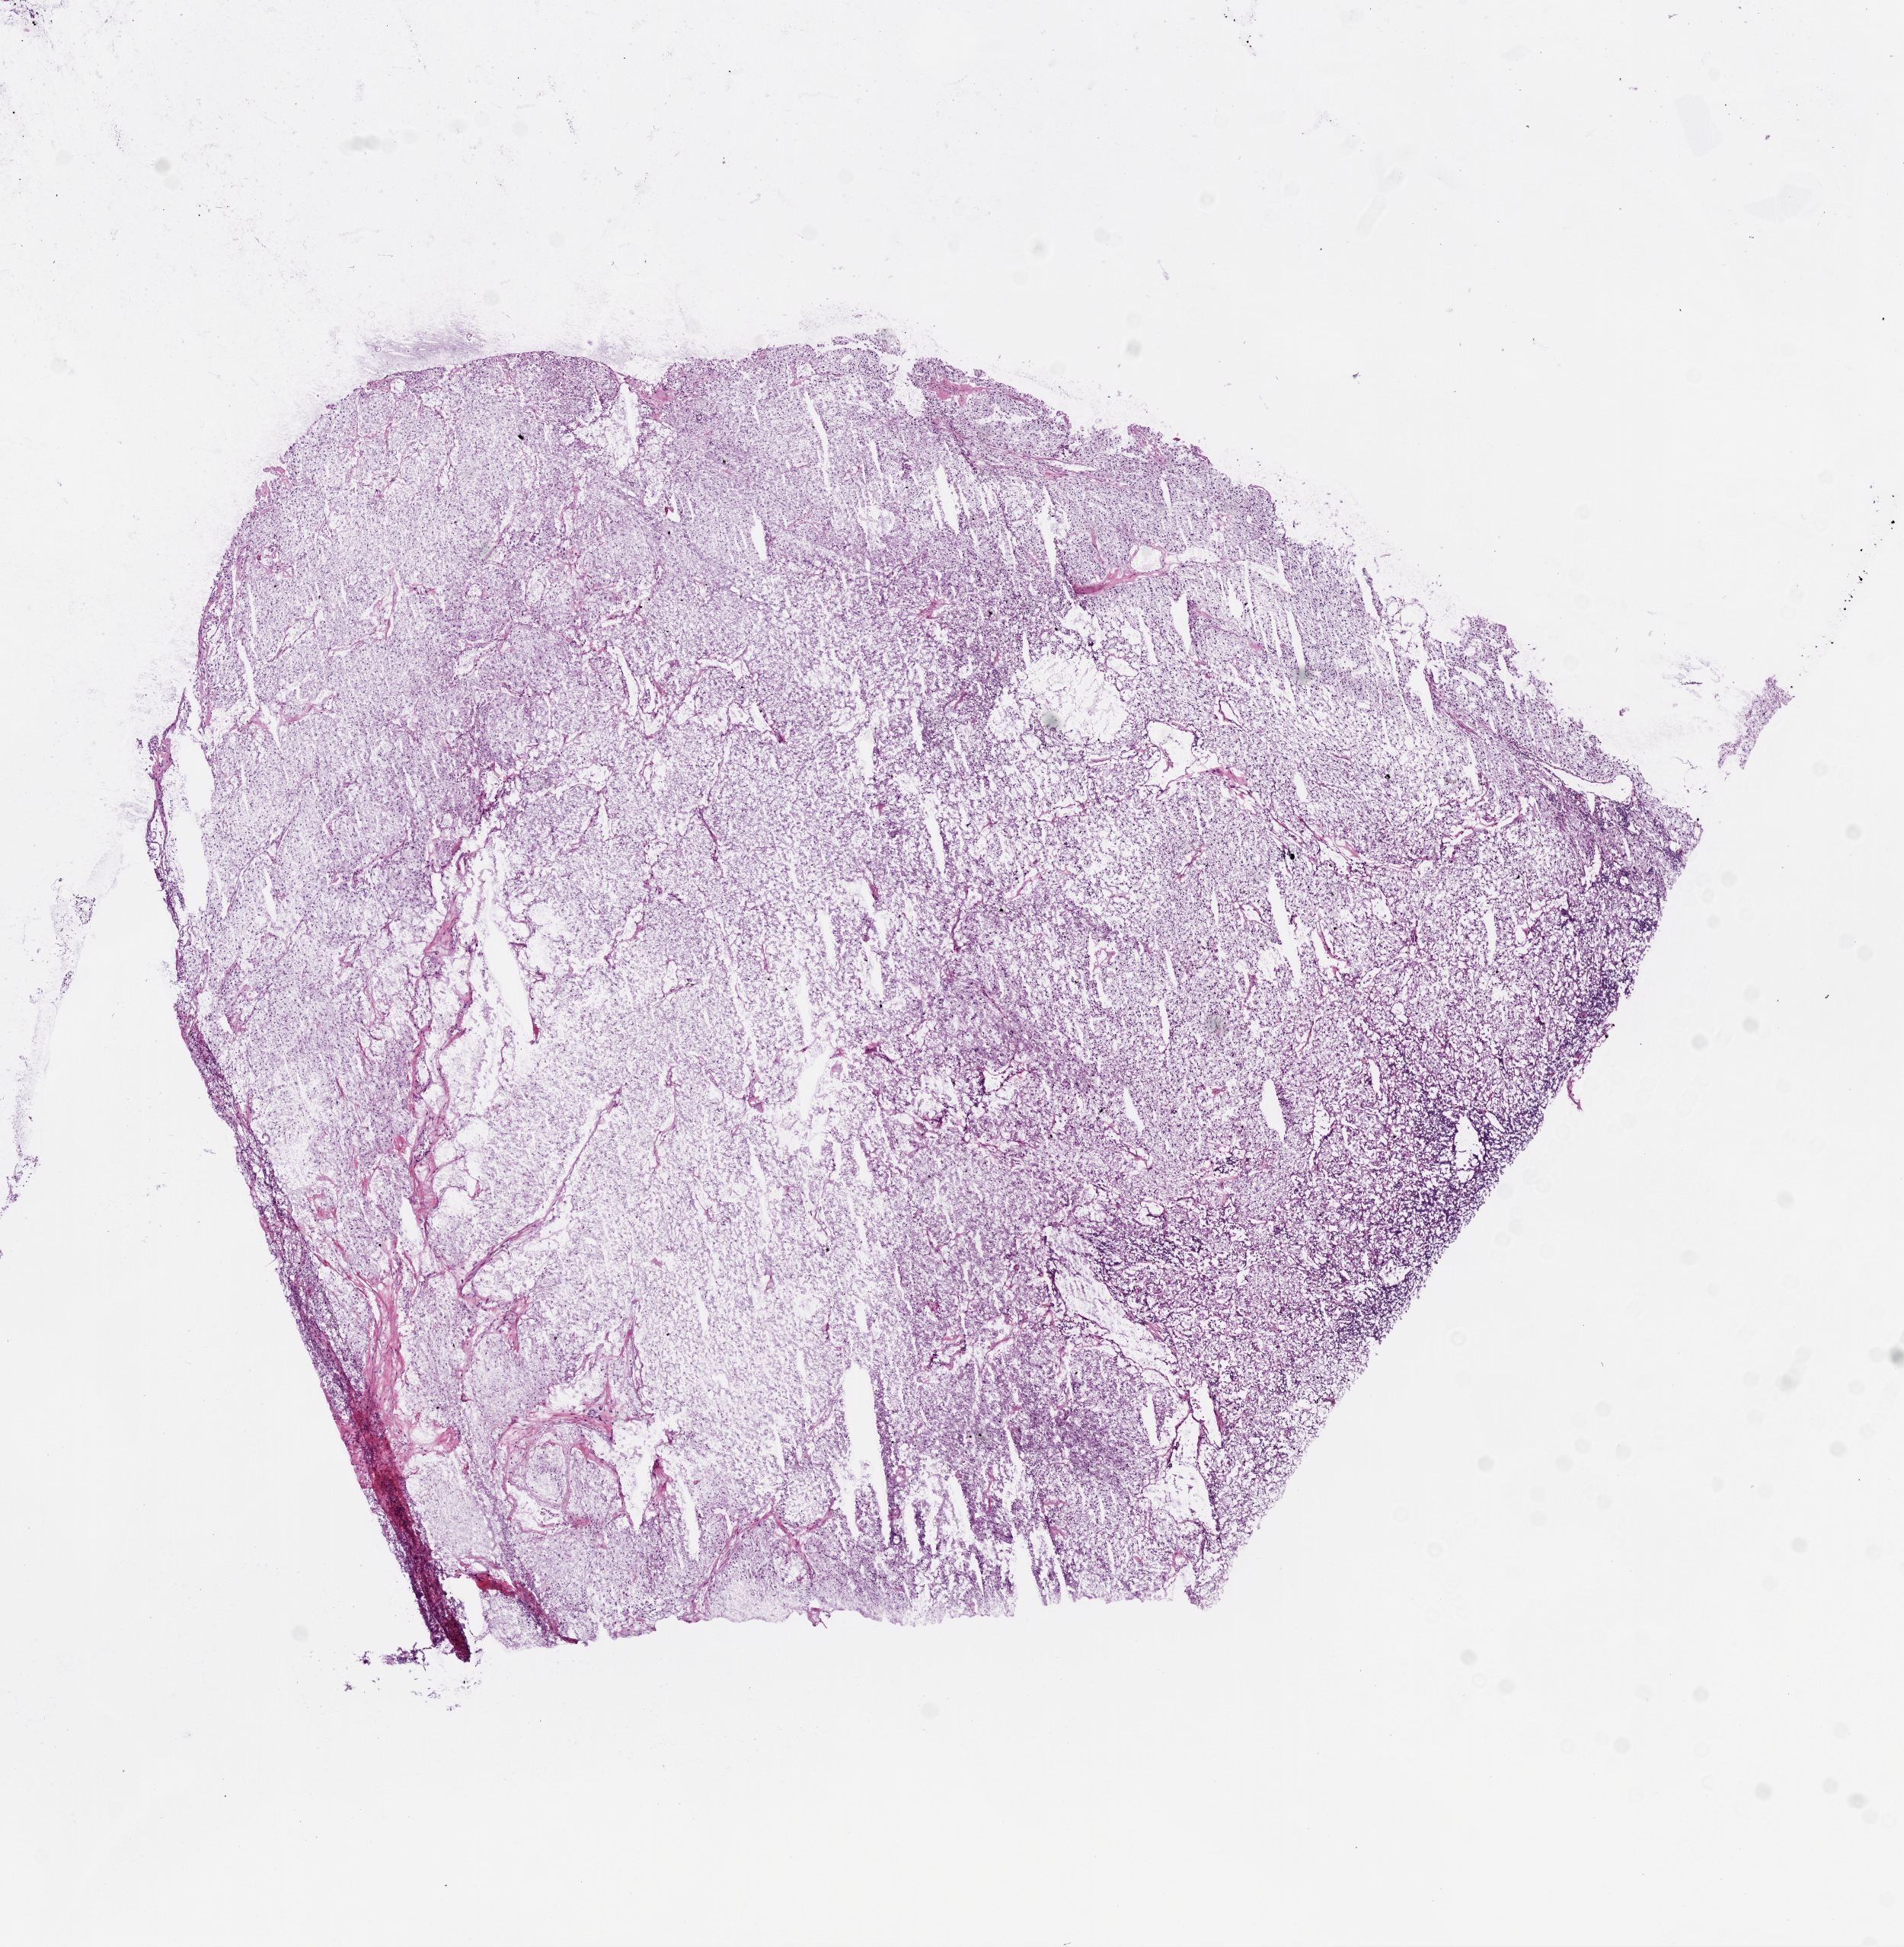
Digitized H&E-stained tissue section (whole slide) — a low-resolution overview of the entire scanned area, about 10.0 x 10.3 mm (acquisition: 20x scan). Frozen section from the top of the tissue portion. Primary tumour sample from the kidney. Male, age 45 years at initial diagnosis. Histologic grade: G2 (moderately differentiated). Slide review estimates, as recorded: tumour cells 95%, tumour nuclei 80%, normal cells 0%, stromal cells 5%, necrosis 0%. Infiltration values recorded for this section: lymphocyte infiltration 10%, monocyte infiltration 0%, neutrophil infiltration 0%.
Diagnosis: Clear cell adenocarcinoma, NOS. AJCC pathologic stage: II. Laterality: left.